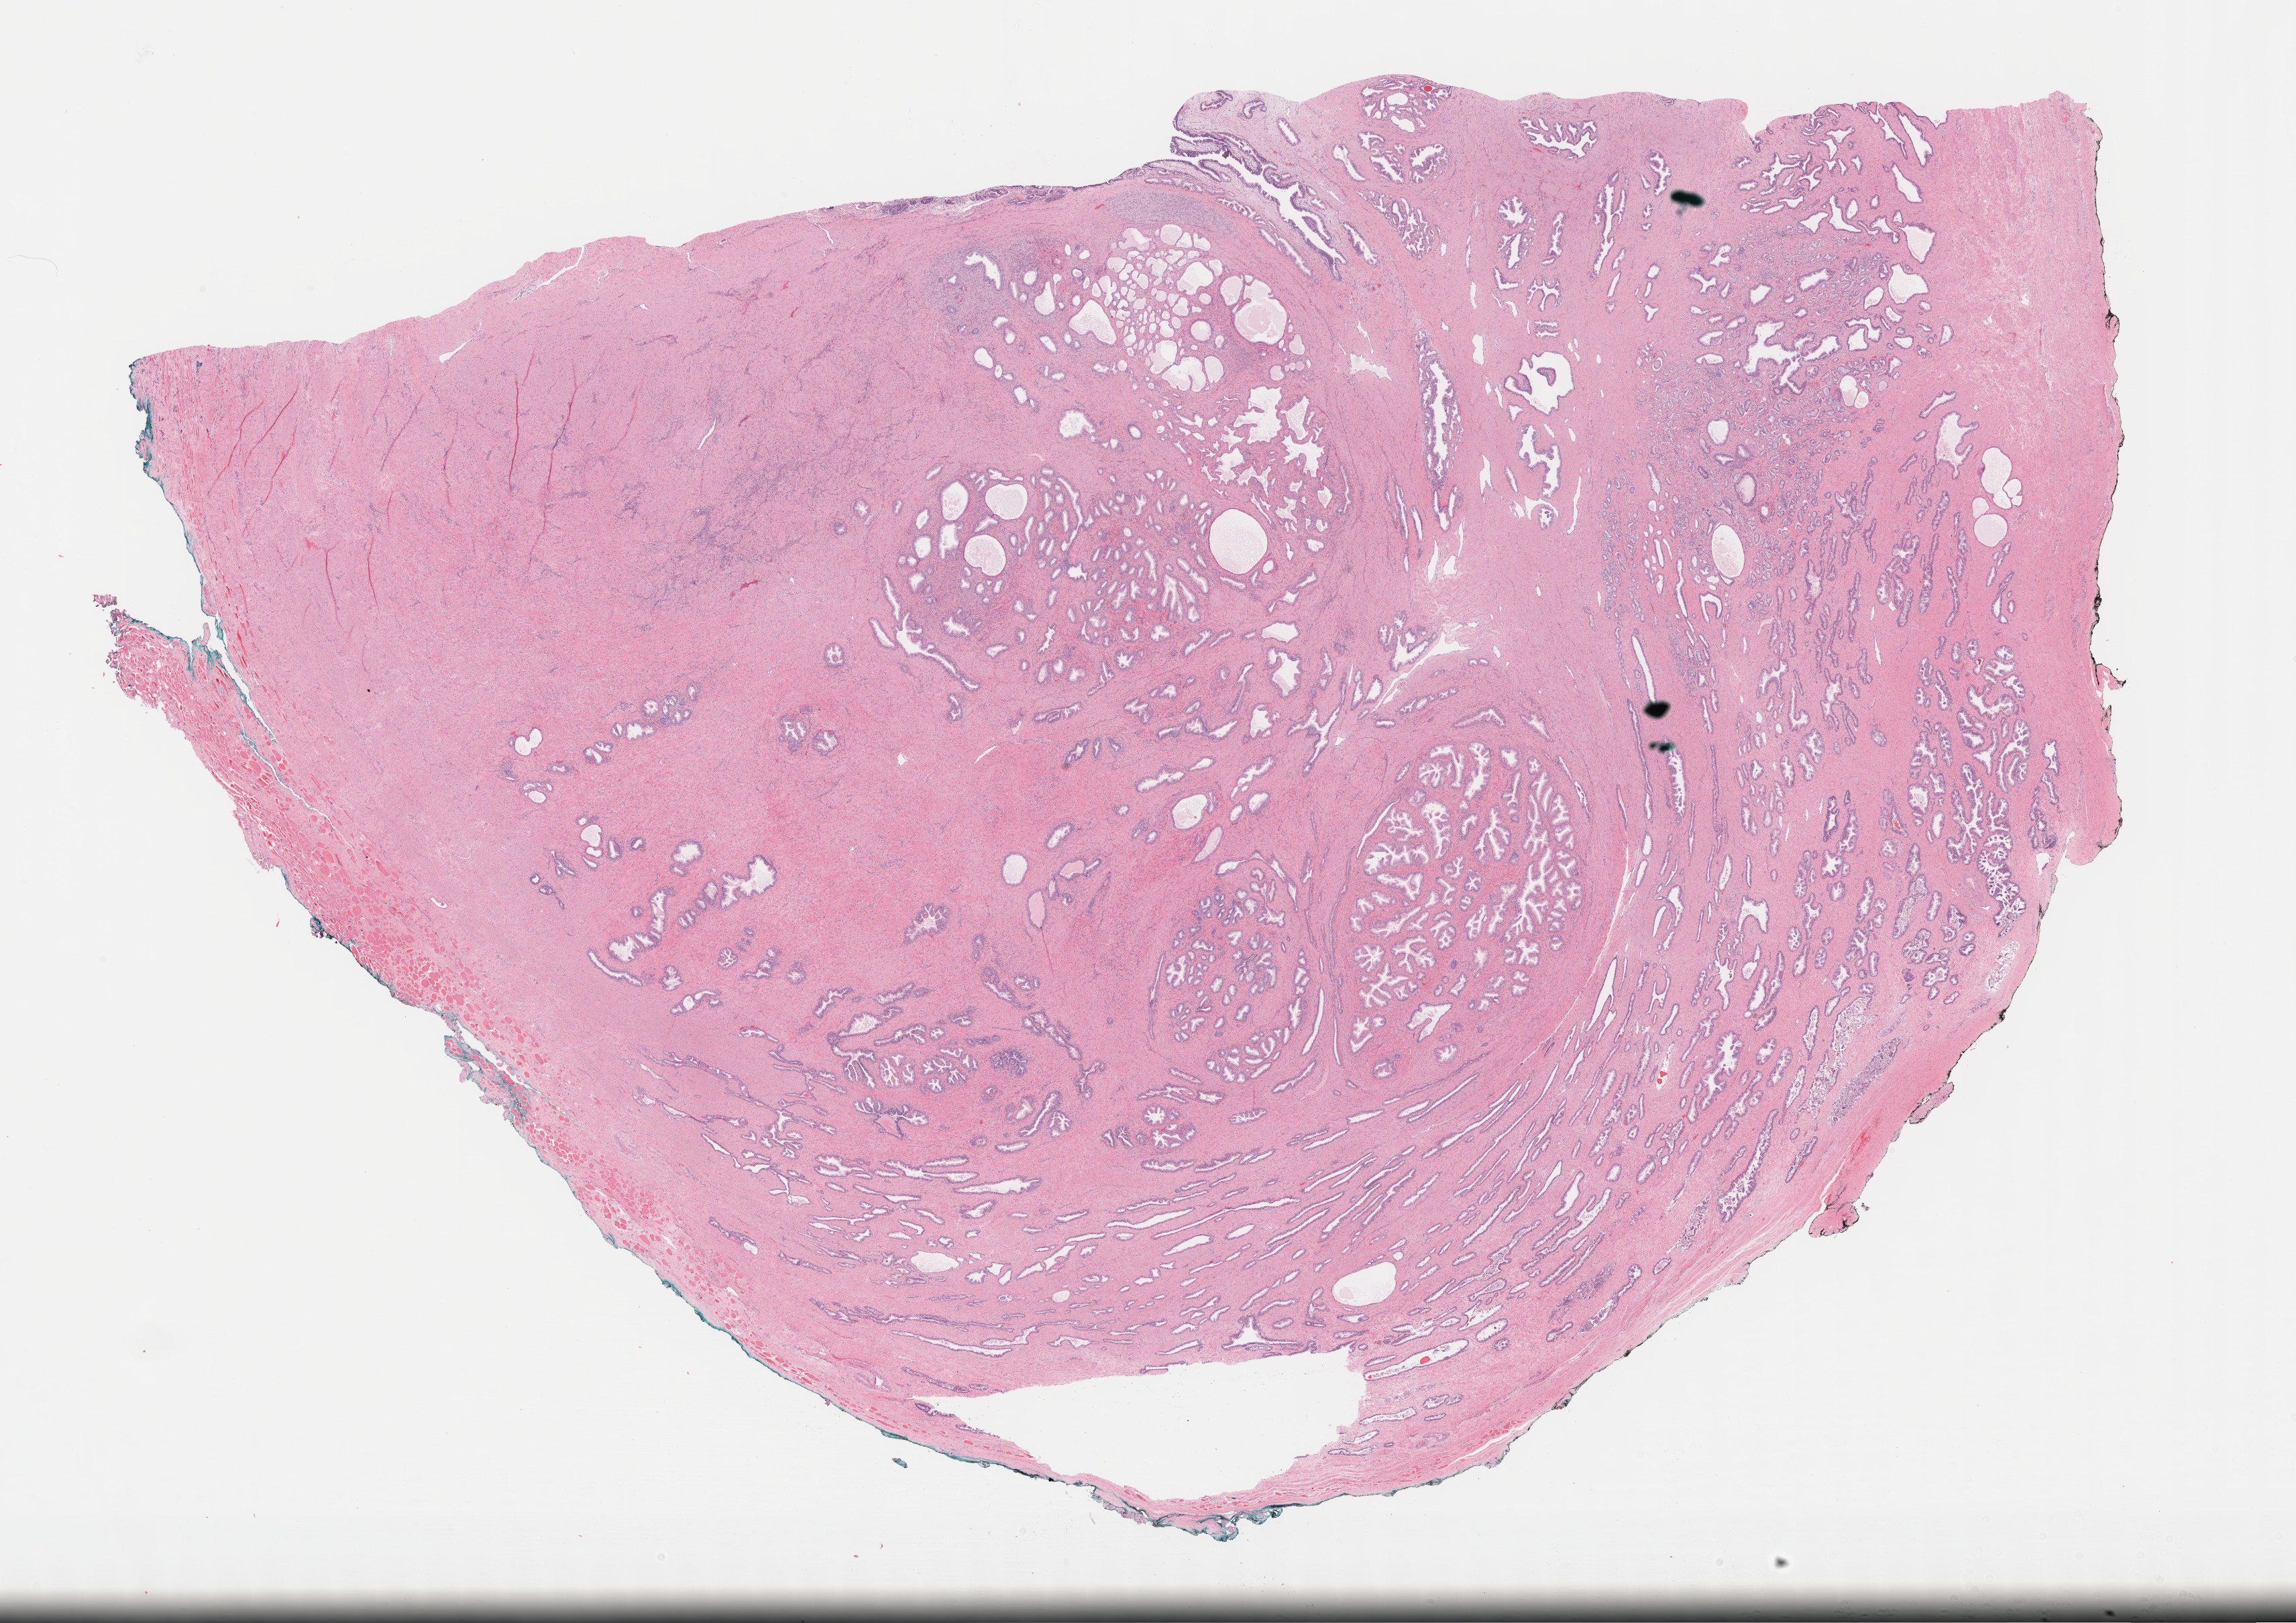
Whole-slide histology image, Hematoxylin and eosin (H&E) stained — low-resolution overview of the scanned area, about 27.7 x 19.6 mm (from a 40x scan), formalin-fixed paraffin-embedded (FFPE) diagnostic section, prostate, primary tumour sample. Patient: male, age at initial diagnosis 47 years. Gleason score: 6 (3+3).
• histologic diagnosis: Adenocarcinoma, NOS (prostate gland)